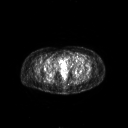
FDG PET of an extremity soft-tissue mass (from a PET/CT study), one axial slice; slice 53 of 267 in the series (ordered by position); 128 × 128 image matrix, field of view 700 × 700 mm. Patient: female, 47 years. Case-level facts recorded for this patient, not image findings: histological type: myxofibrosarcoma; grade: intermediate; site of the primary tumour: left thigh.
Outlined on this slice (expert contour drawn on MRI and transferred to this co-registered scan by the dataset authors):
- gross tumour volume including surrounding oedema: bounding box <66,57,82,63> (left, top, right, bottom; pixels)